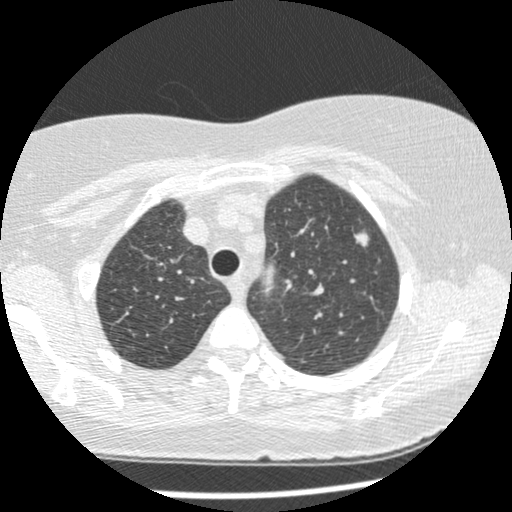
Low-dose screening chest CT, one axial slice; position 186 of 241 along the scan axis; reconstruction kernel STANDARD; lung window (W 1500 / L -600 HU); 1.25 mm slice thickness; 512 × 512 image matrix.
Annotated regions visible in this slice (outlined manually by an expert reader):
- lesion 2 (tumor, upper lobe of left lung): box from (x=354, y=230) to (x=370, y=247) px